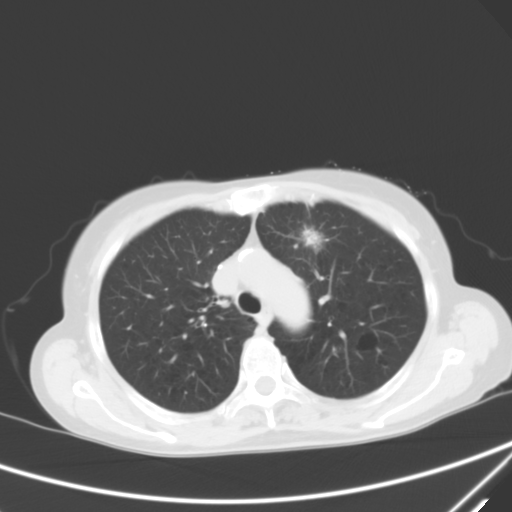
Chest CT, one axial slice. Position 45 of 60 along the scan axis. 120 kVp. Lung window (W 1500 / L -600 HU). 5 mm slice thickness. 512 × 512 image matrix, field of view 350 × 350 mm. Female patient, age 71 years. From the clinical record (not read from this slice): clinical TNM (as recorded): T1c N0 M0; histopathological grade: G2-3.
Annotated regions visible in this slice (bounding box drawn by a radiologist):
- lung tumour (recorded histology: adenocarcinoma): bounding box [x1, y1, x2, y2] px = [298, 221, 328, 257]